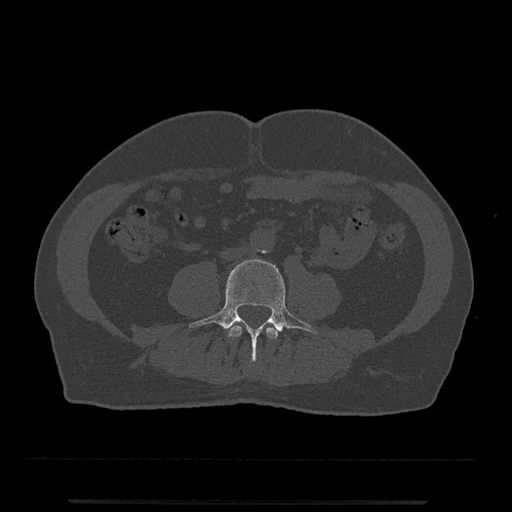
CT including the spine, one axial slice. Position 149 of 797 along the scan axis. Reconstruction kernel Br40s/3. 120 kVp. Bone window (W 1800 / L 400 HU). 0.5 mm slice thickness. 512 × 512 image matrix, field of view 419 × 419 mm. Male patient, age 63 years. Case-level facts recorded for this patient, not image findings: primary cancer: prostate.
Structures marked on this image (semi-automatic segmentation, software-assisted and operator-edited):
- L3 vertebra: bounding box [x1, y1, x2, y2] px = [228, 324, 278, 339]
- L4 vertebra: [189, 259, 319, 365]